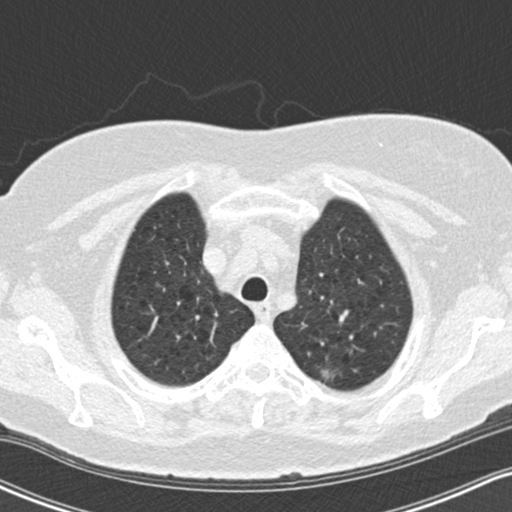
Low-dose screening chest CT, one axial slice; position 133 of 155 along the scan axis; lung window (W 1500 / L -600 HU); 2 mm slice thickness; 512 × 512 image matrix.
Outlined on this slice (manually delineated by an expert):
- lesion 1 (tumor, upper lobe of left lung): bounding box <321,369,331,379> (left, top, right, bottom; pixels)